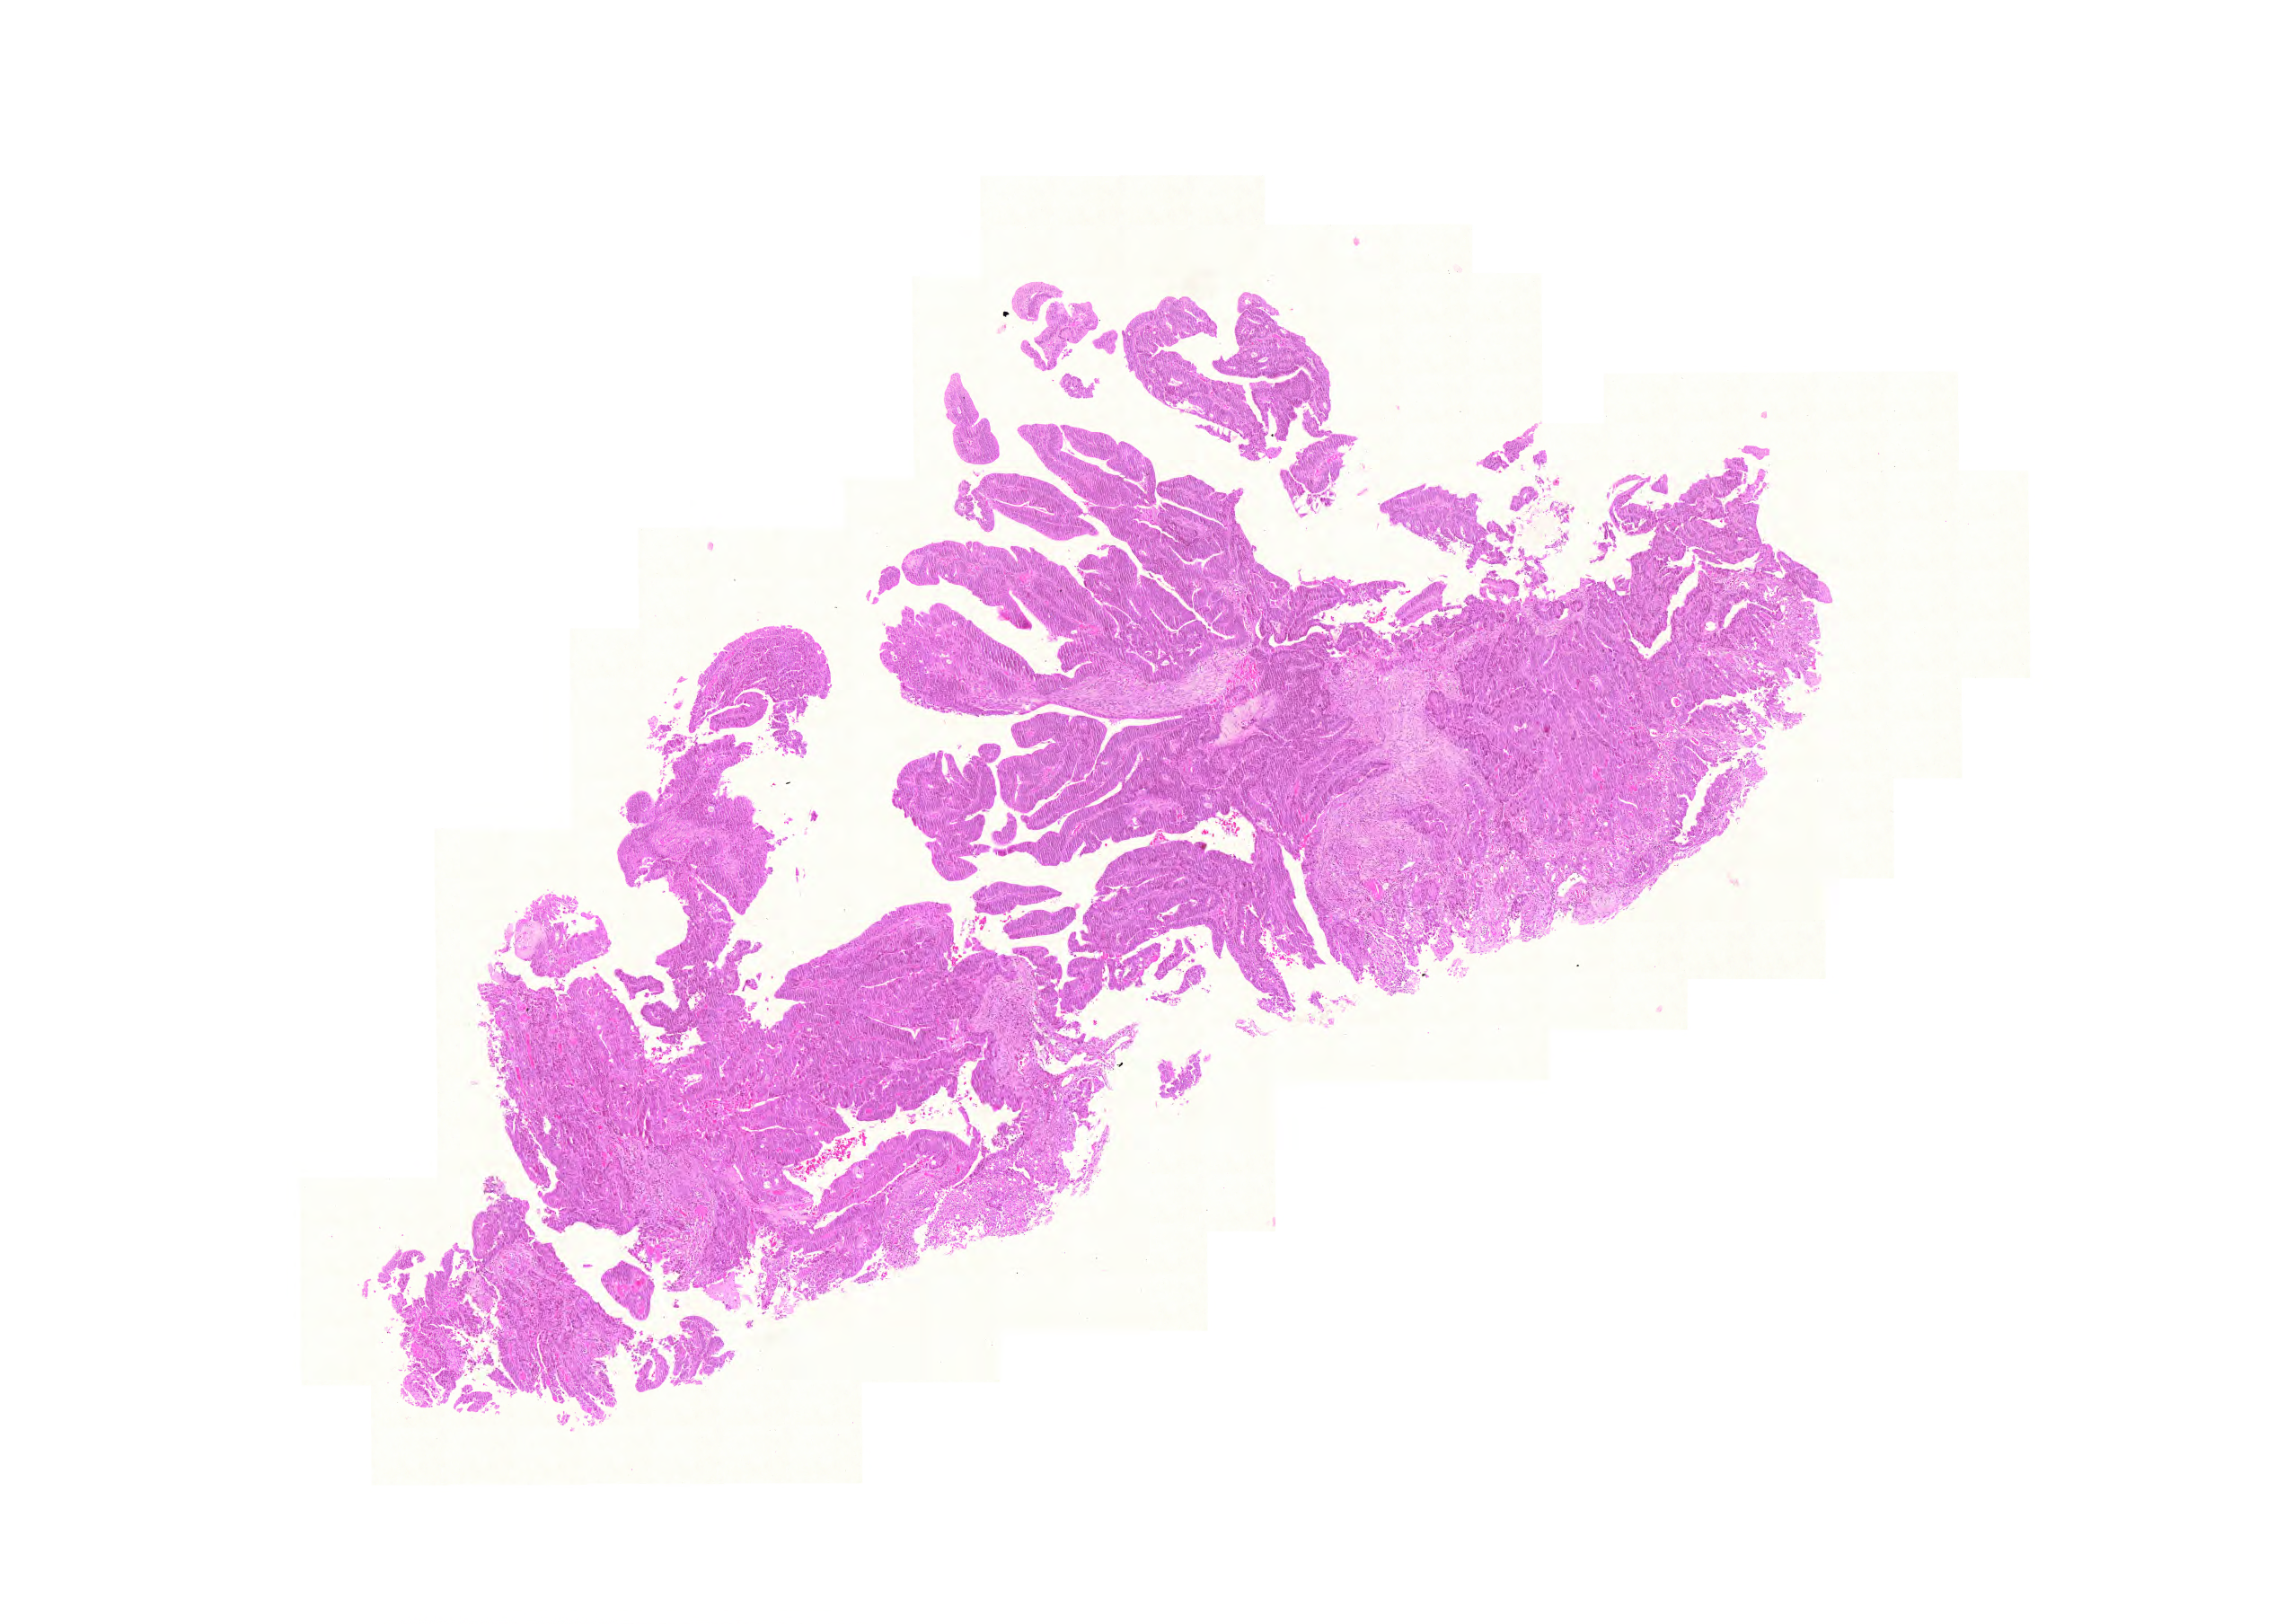
H&E whole-slide image — whole scanned area (about 9.5 x 6.7 mm, from a 20x scan) shown as a low-resolution overview; formalin-fixed paraffin-embedded (FFPE) diagnostic section; sample: primary tumour, rectum. Female, age 63 years at initial diagnosis.
- histologic diagnosis: Adenocarcinoma, NOS
- AJCC pathologic stage: I (5th edition)